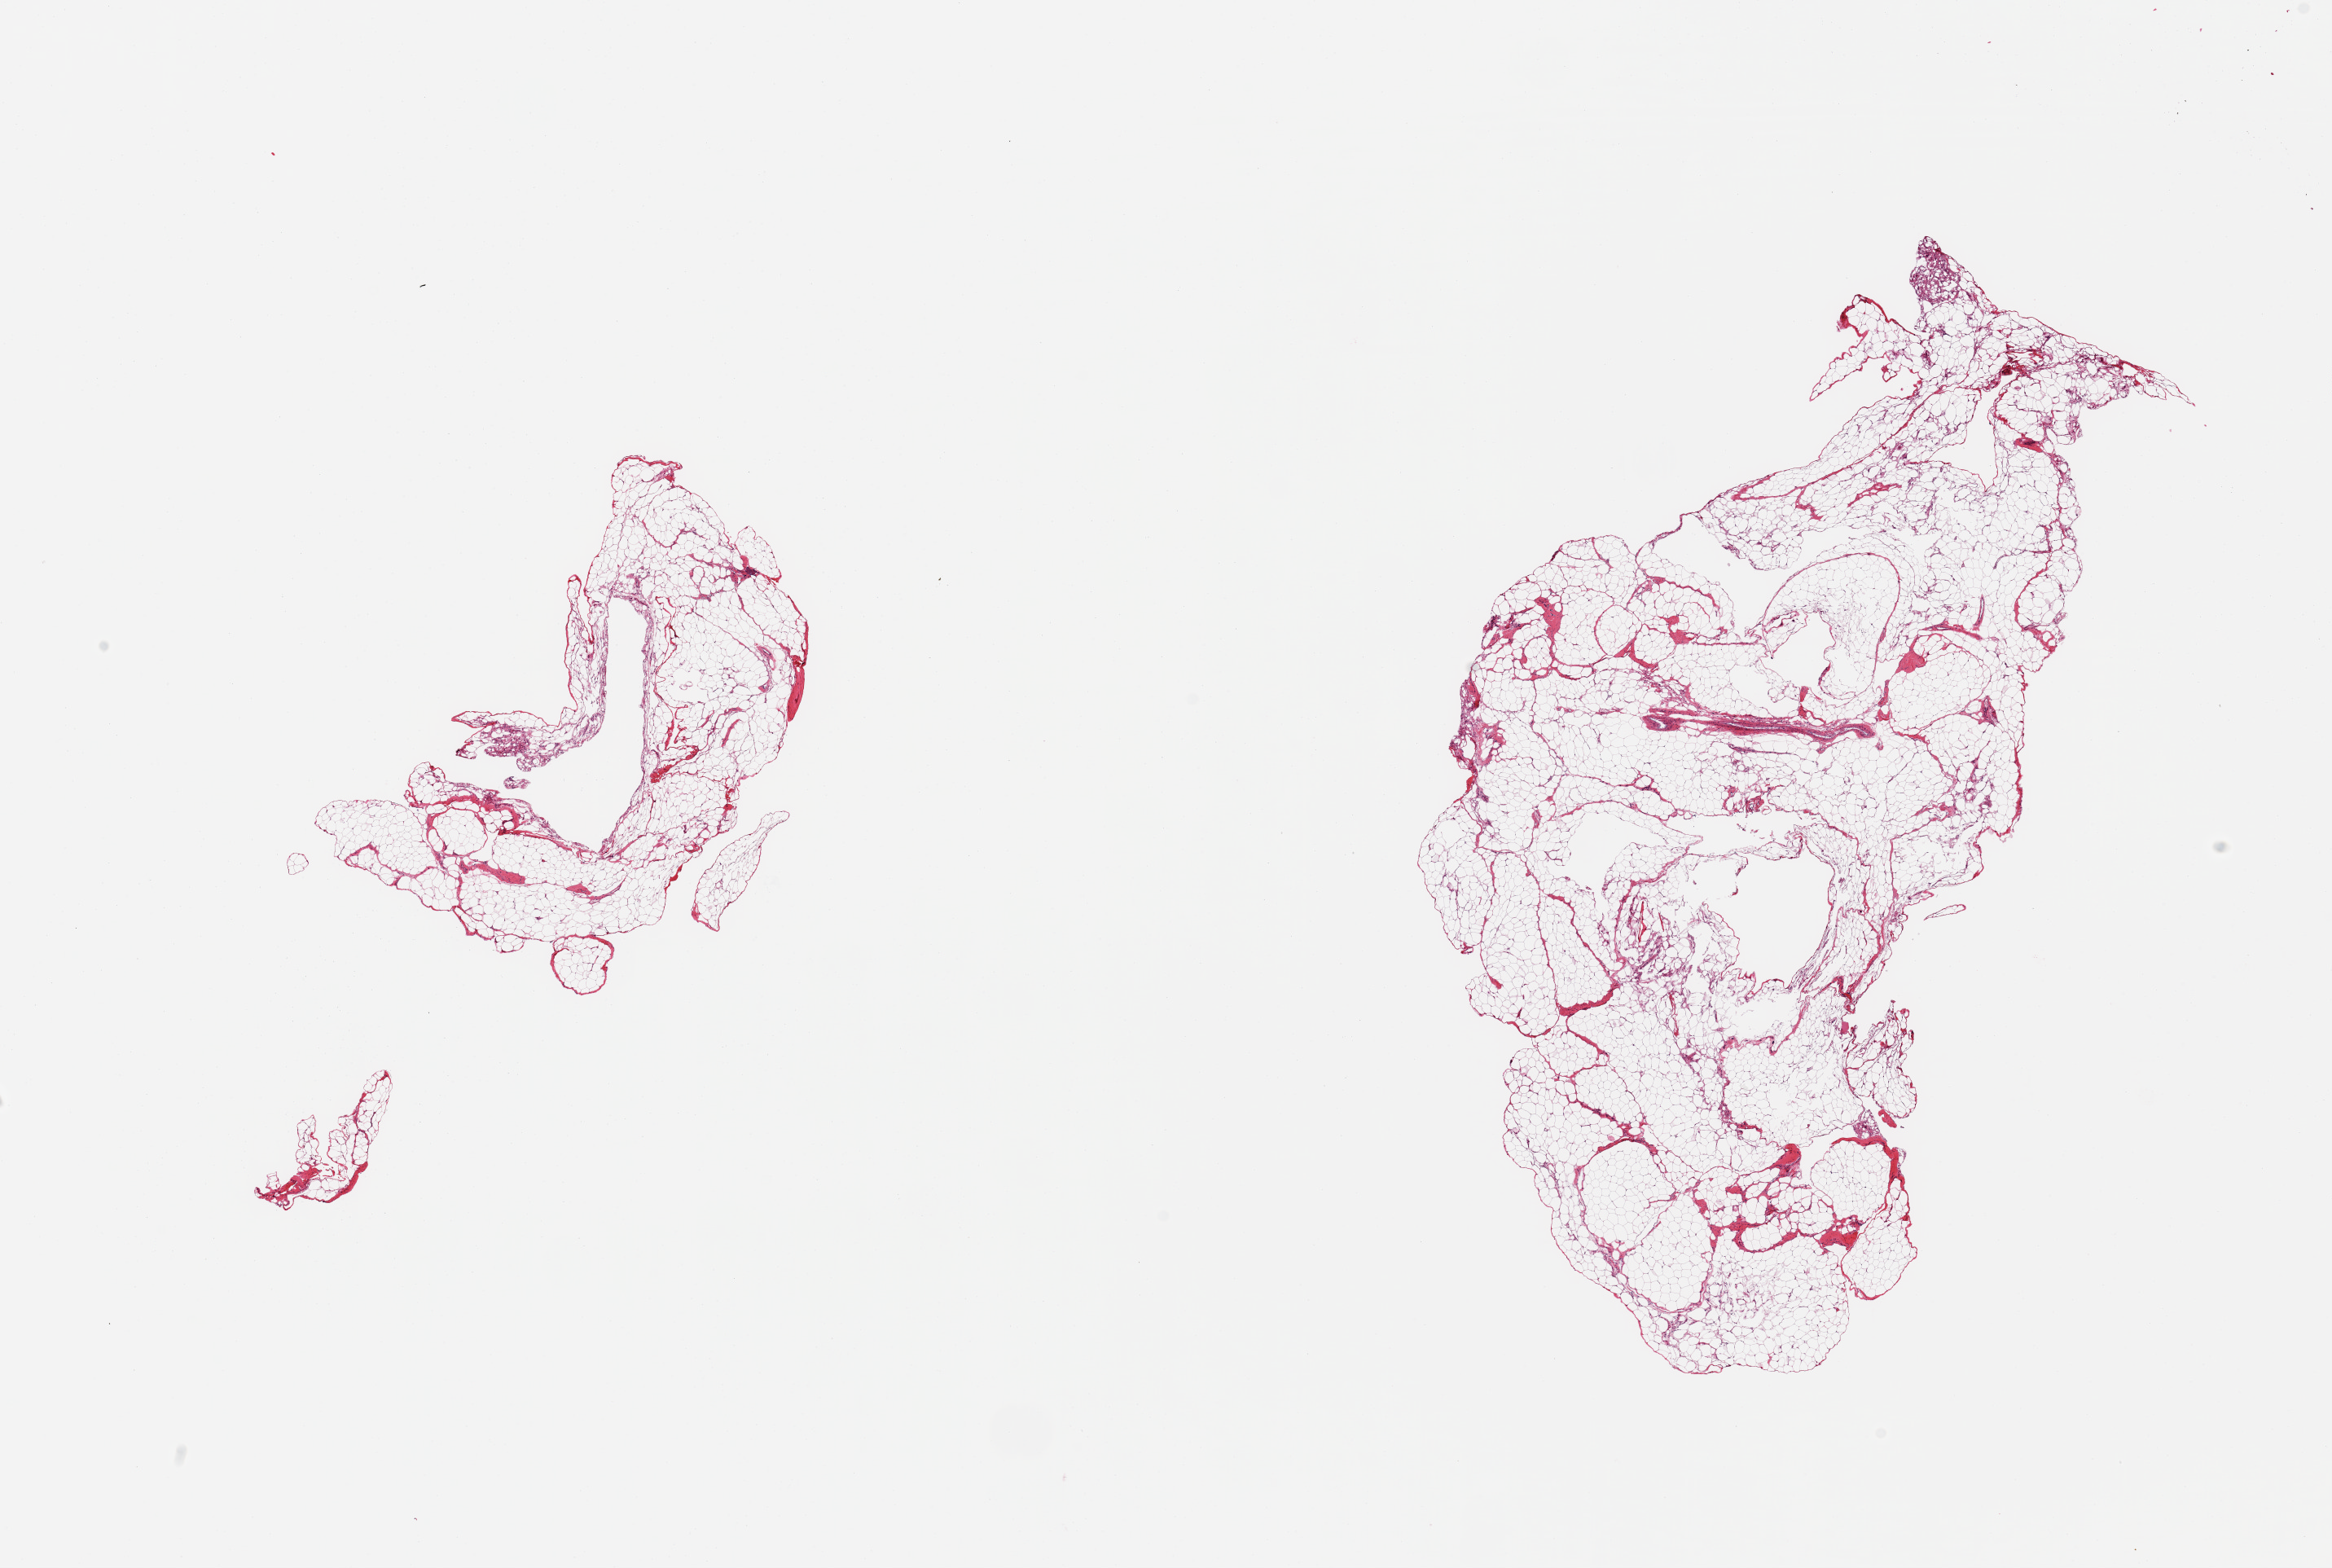
Digitized H&E-stained section, low-resolution overview of the scanned area, about 22.6 x 15.2 mm (from a 20x scan), PAXgene-fixed, paraffin-embedded tissue, section of omentum (target tissue), donor tissue sample. Donor sex: male.
• pathologist's review note for this sample: 2 pieces; mature fat